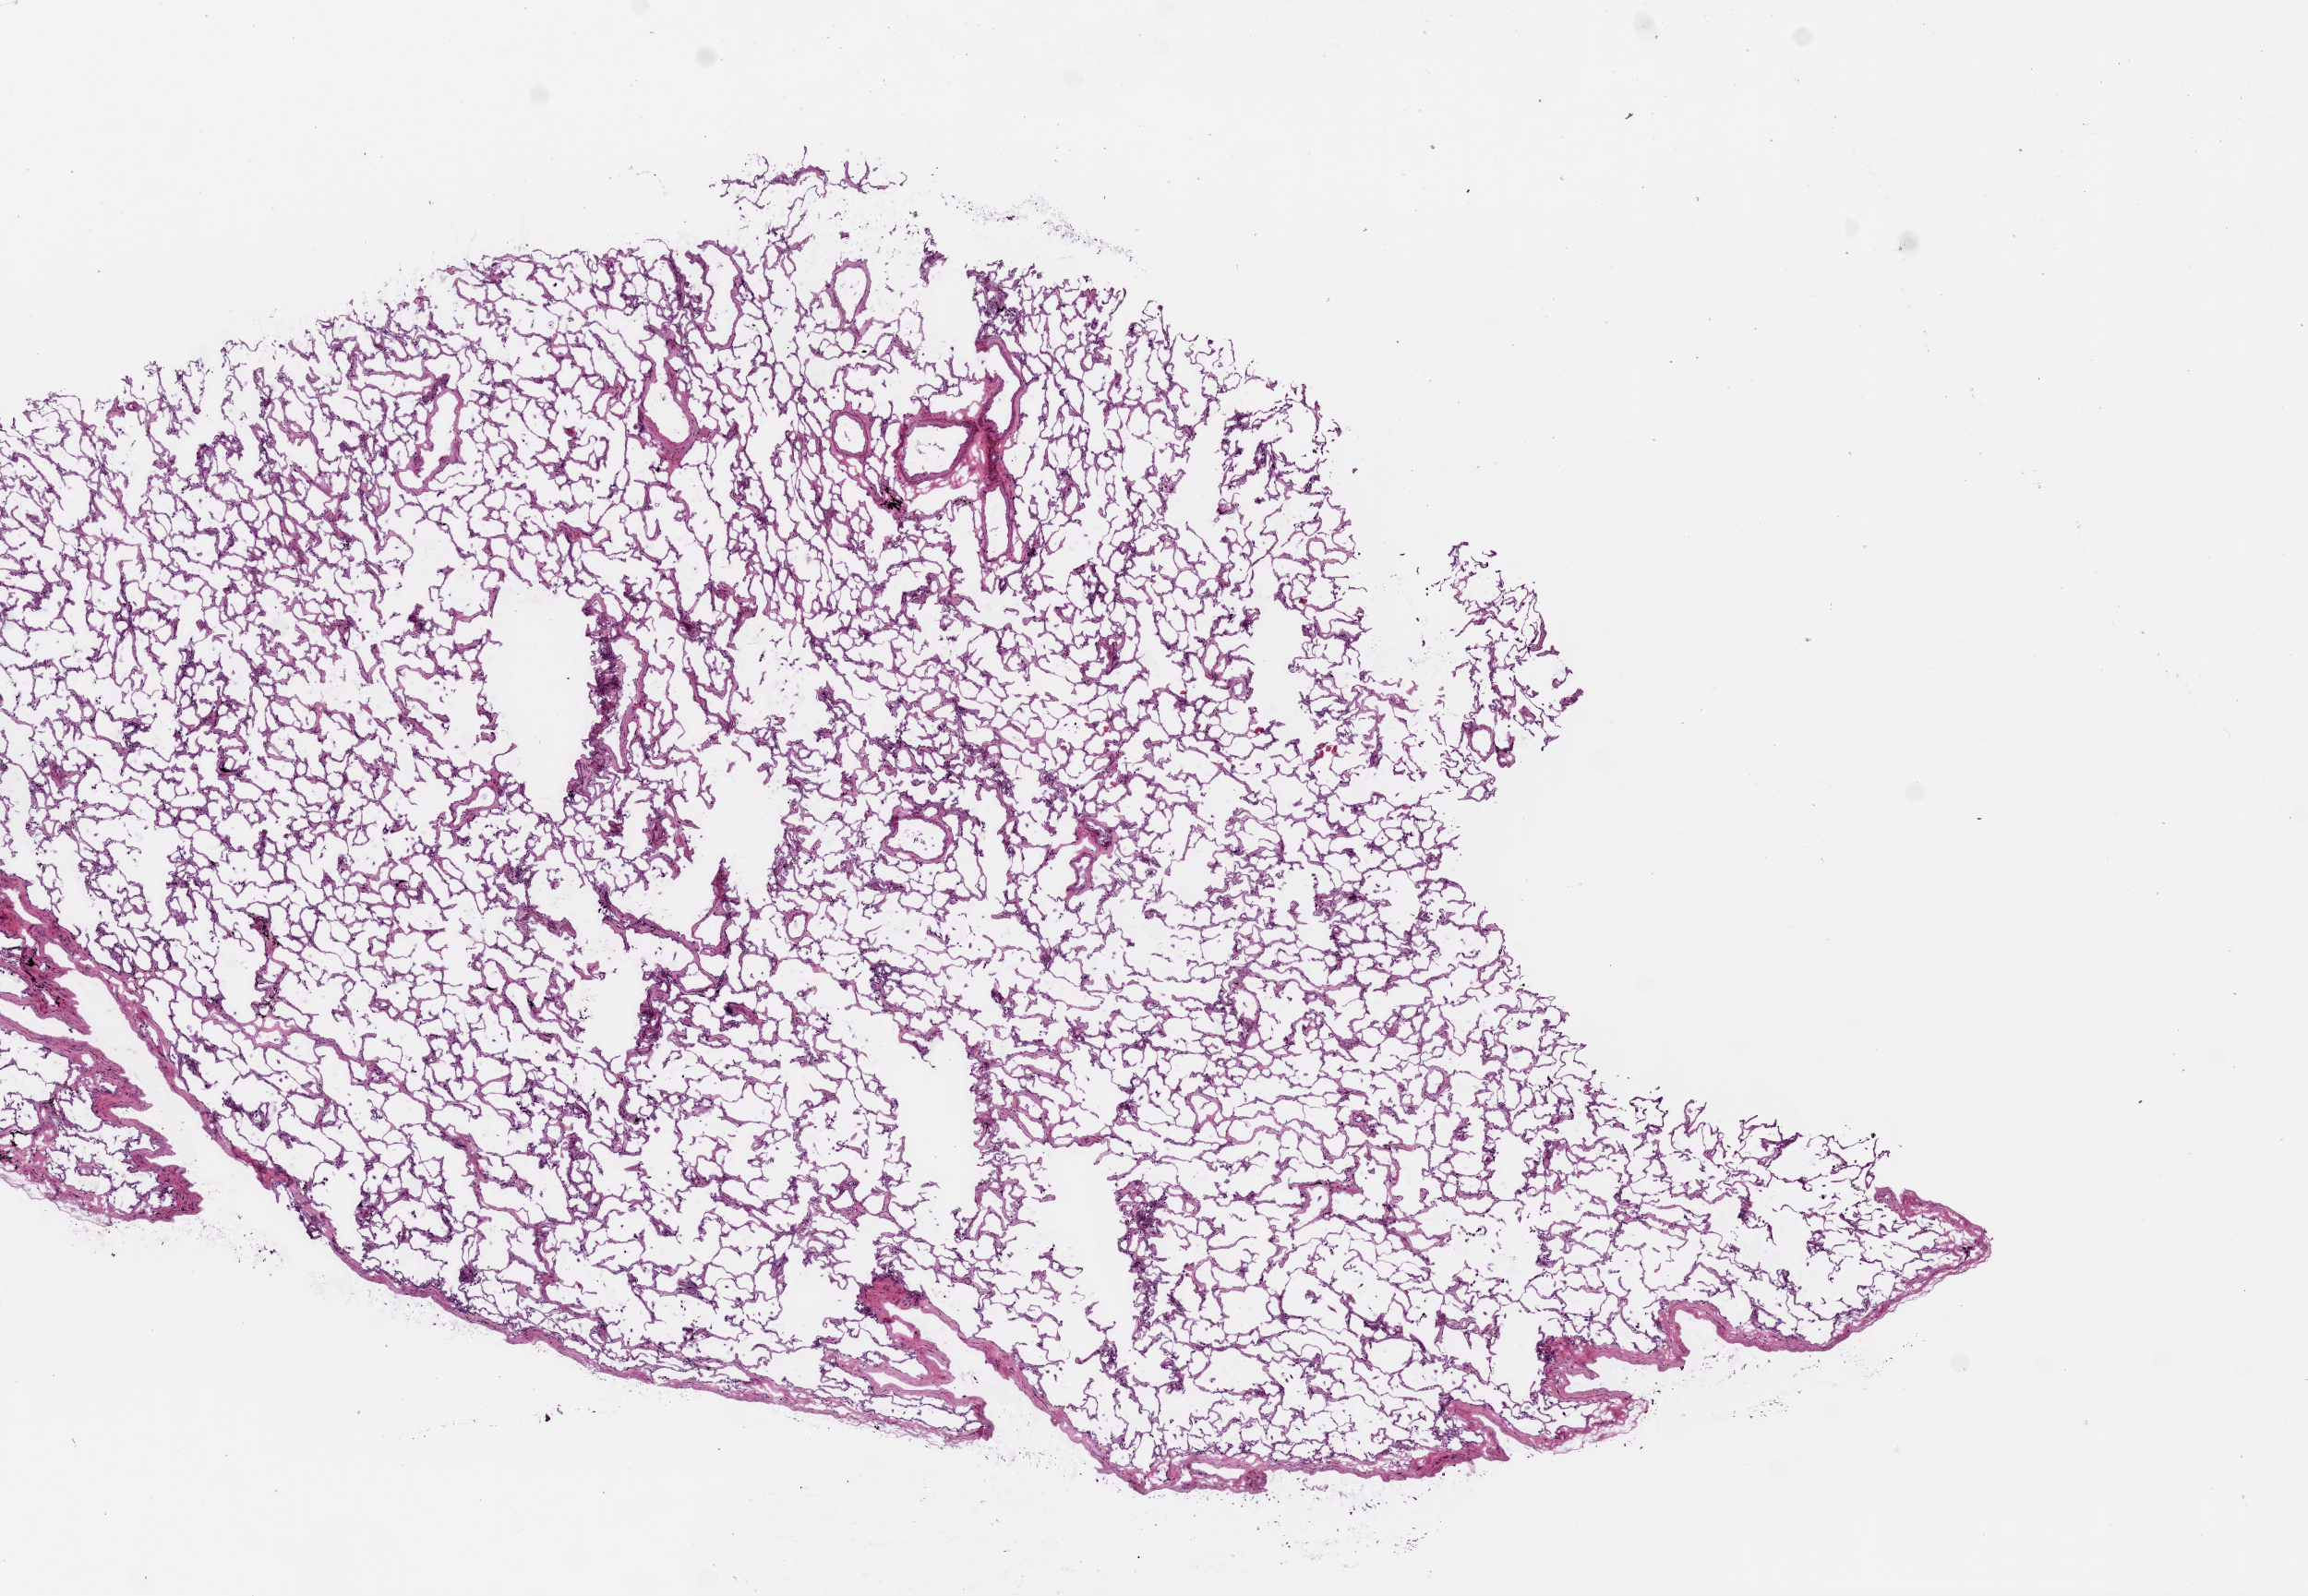
Digitized H&E-stained tissue section (whole slide) — low-resolution overview of the scanned area, about 10.0 x 6.9 mm (from a 20x scan), frozen section from the bottom of the tissue portion, sample: solid tissue normal (non-tumour tissue), lung. Female patient; age at initial diagnosis 73 years.
* this section: solid tissue normal sample (biorepository sample class)
* patient diagnosis: Adenocarcinoma, NOS (main bronchus)